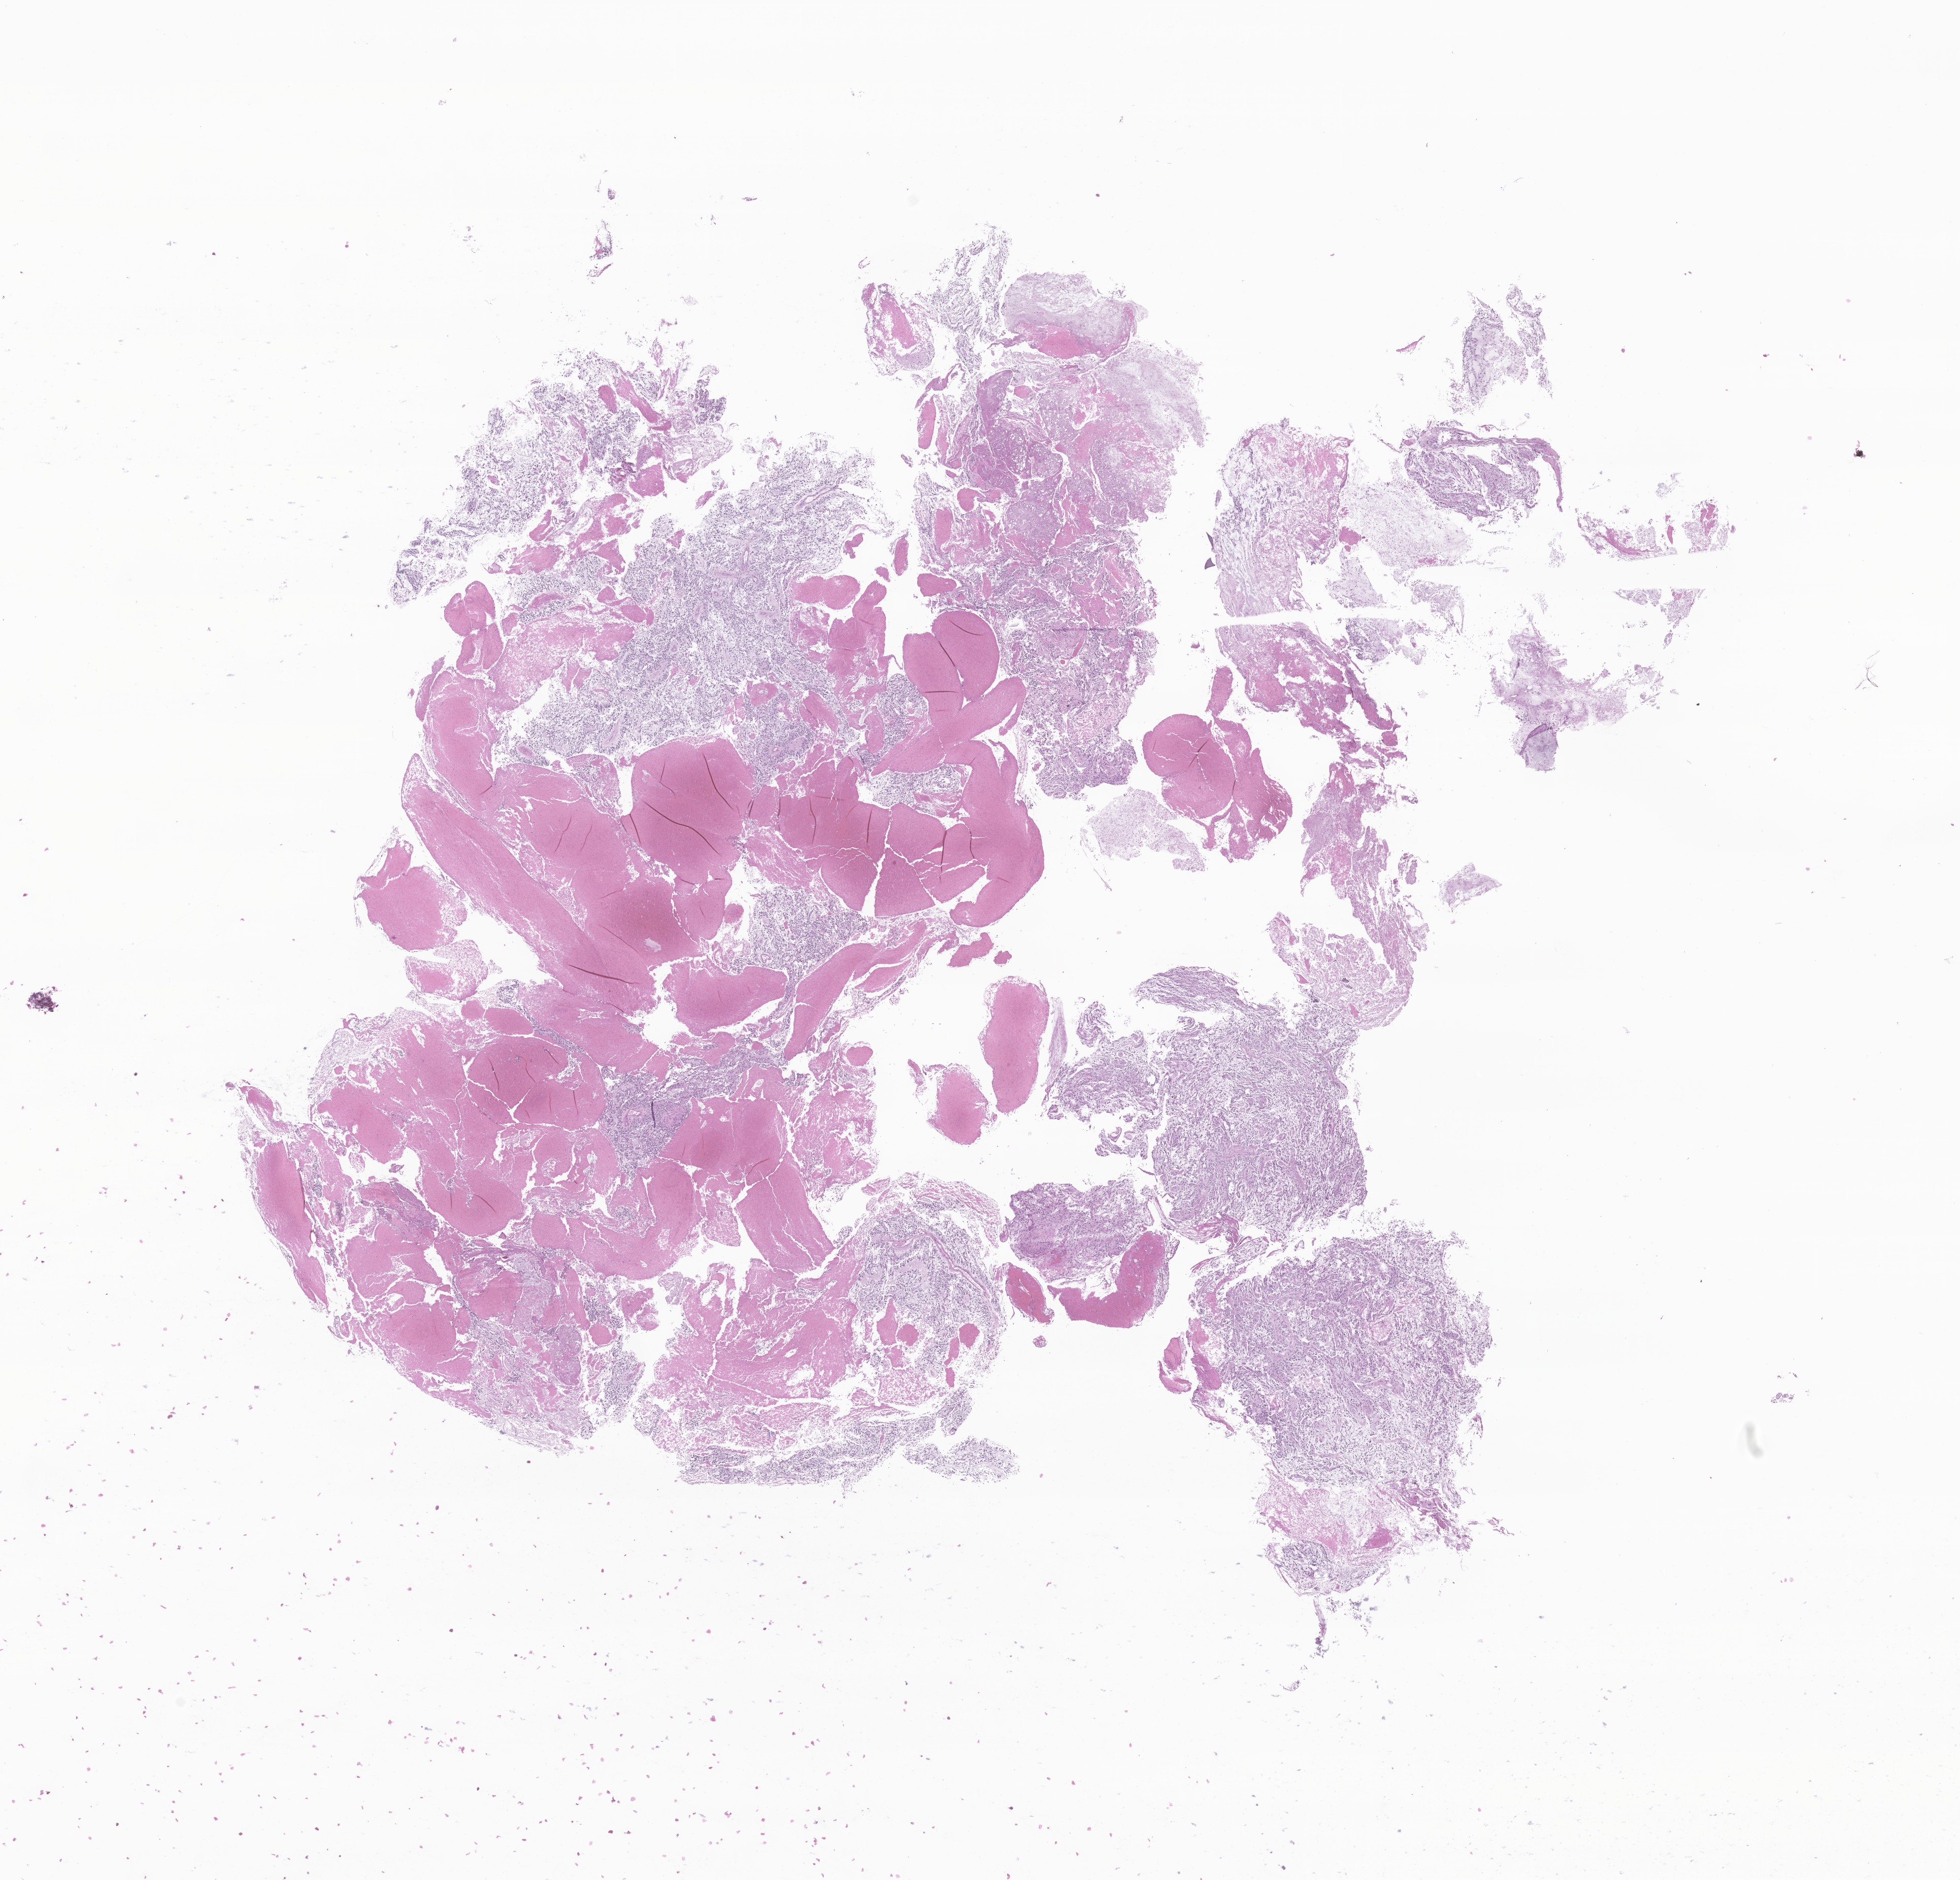
Digitized H&E-stained section of tumor tissue from the frontal lobe, whole scanned area (about 16.3 x 15.6 mm) shown as a low-resolution overview, FFPE section. Patient male; age 71 months.
Diagnosis (ICD-O-3 morphology term): Pilocytic astrocytoma.